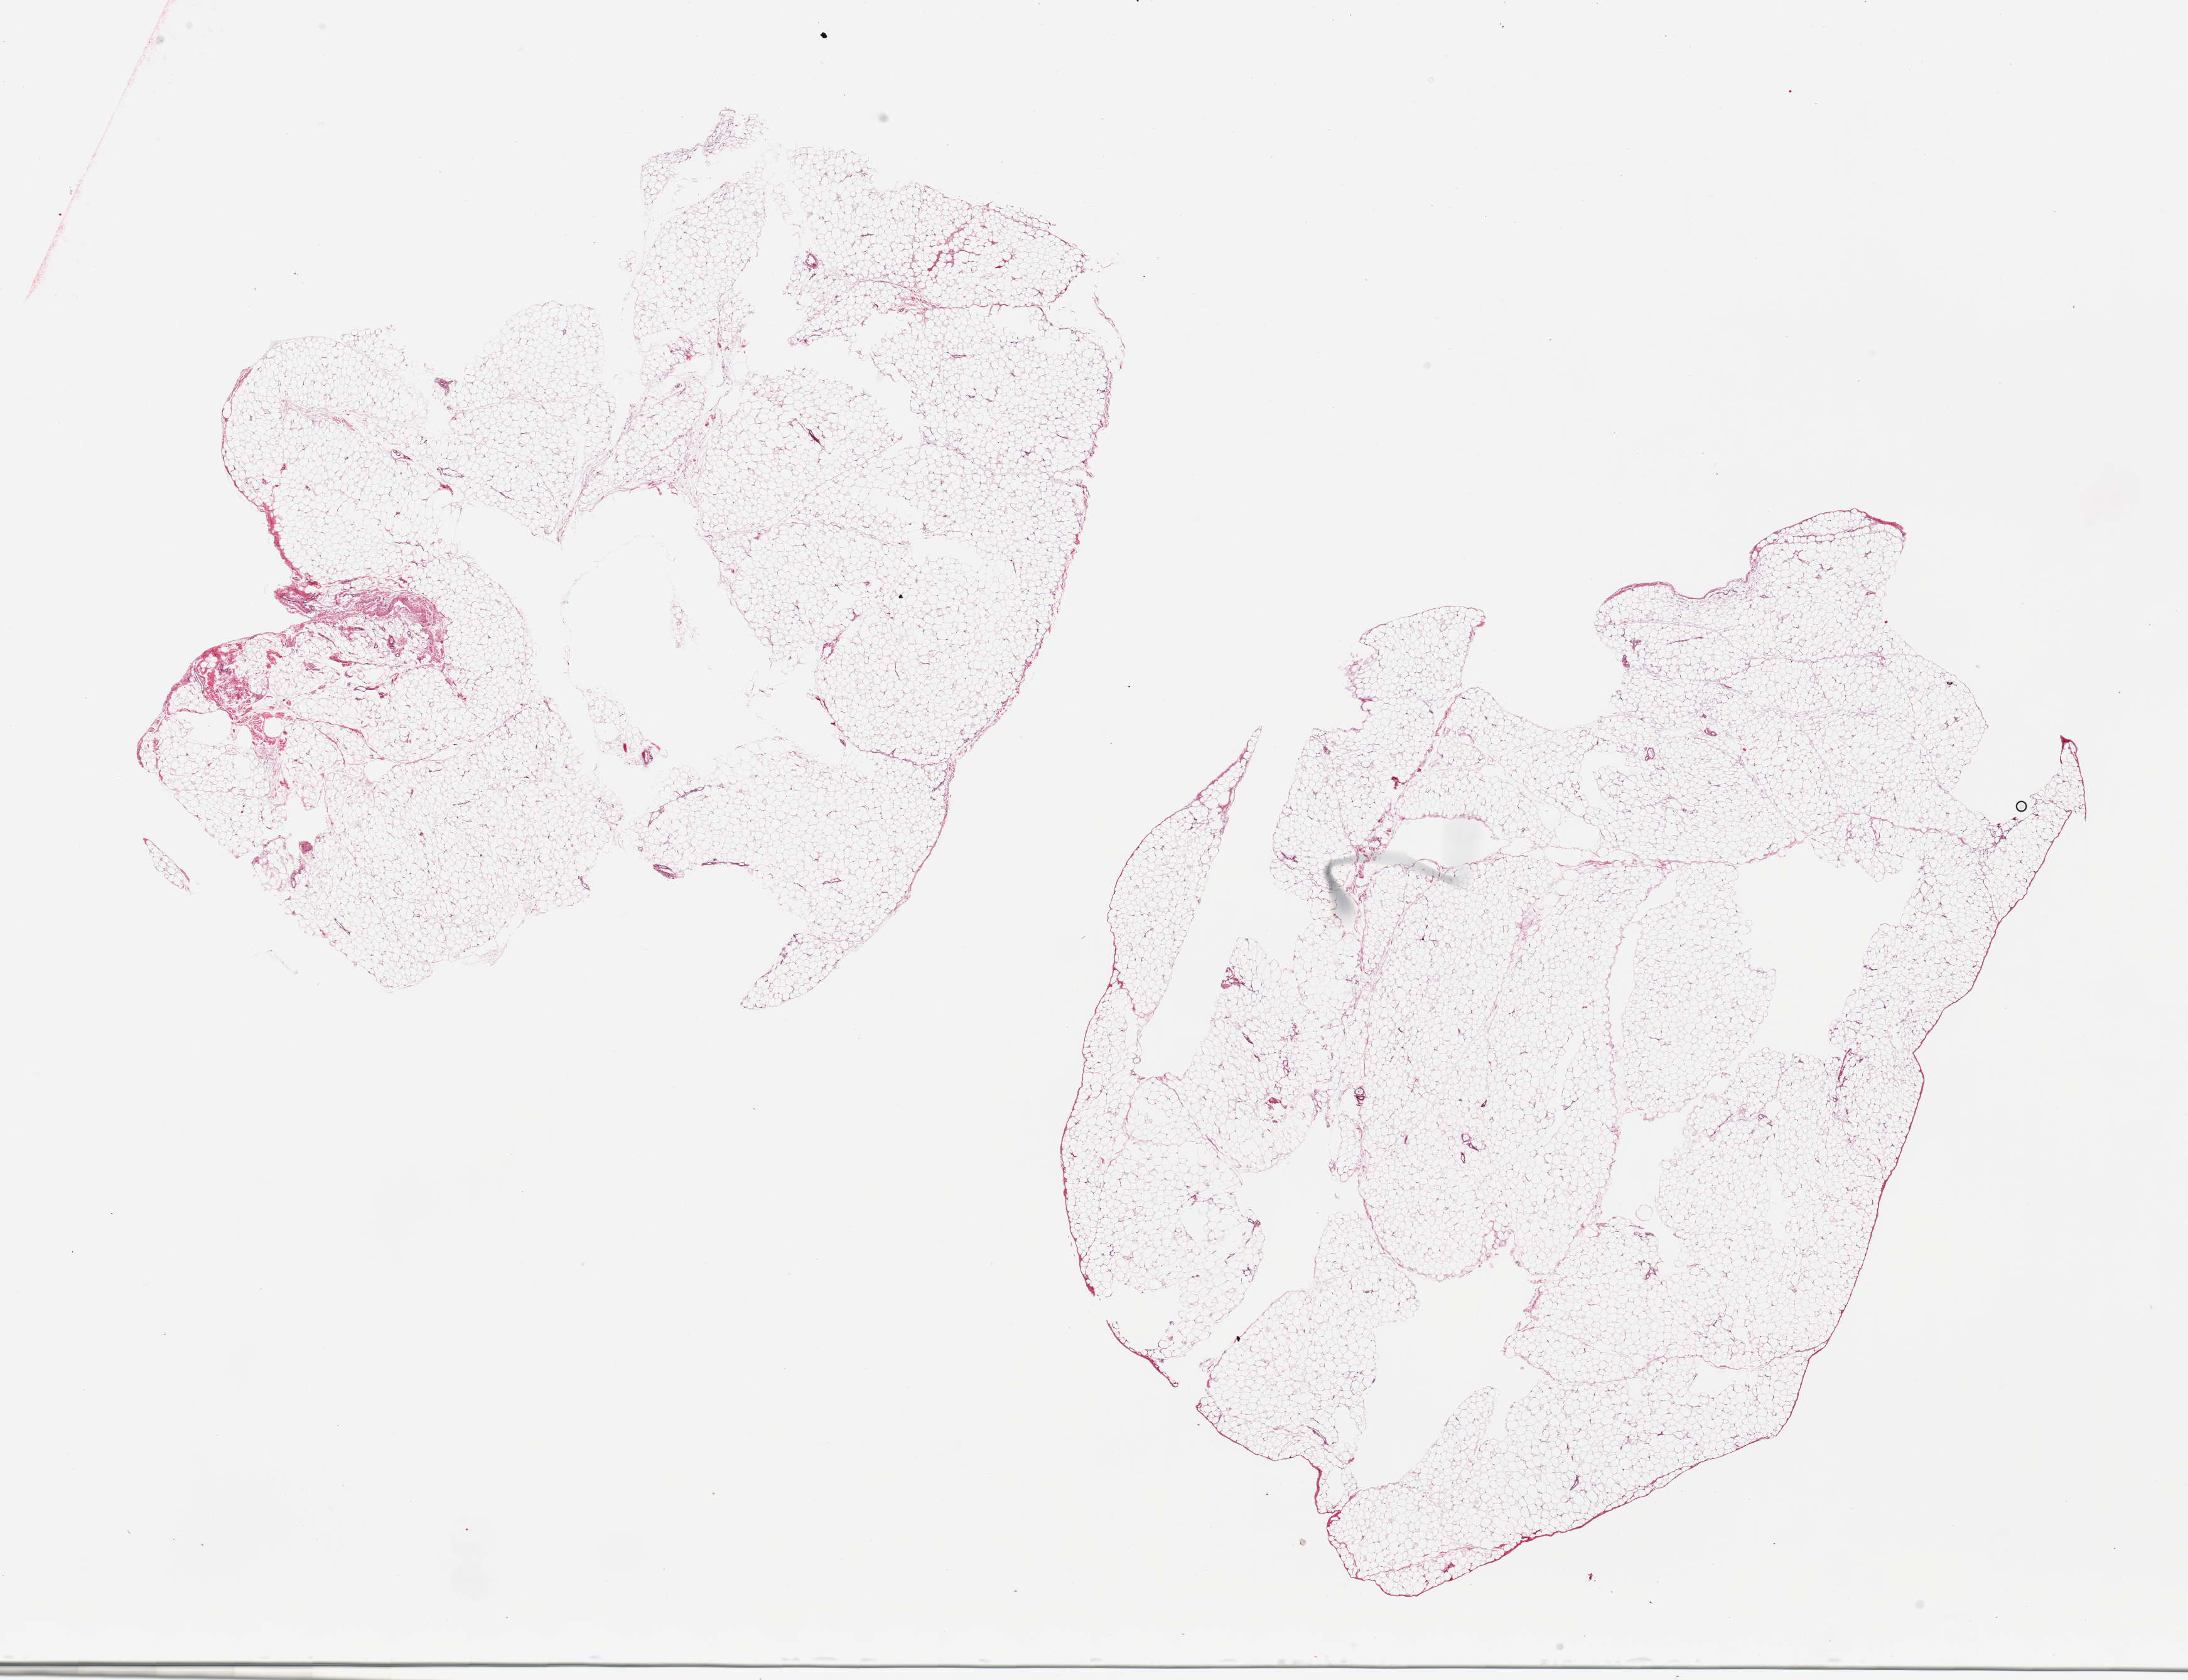
Digitized H&E-stained section, shown as a low-resolution overview of the whole scanned area (about 27.6 x 21.2 mm); PAXgene-fixed, paraffin-embedded tissue; sampled site (target tissue): omentum; tissue donor sample. Donor: male.
Review note (as recorded): 2 pieces.